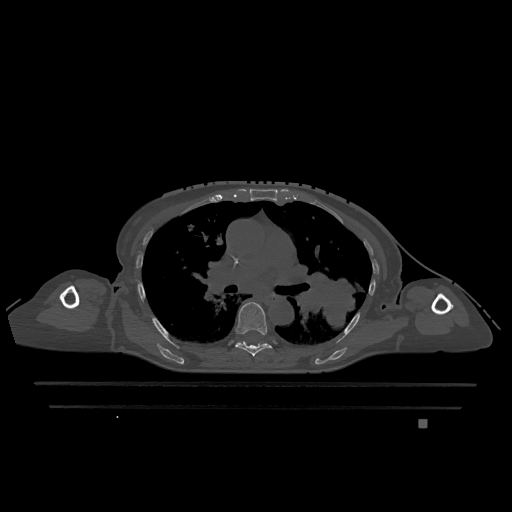
CT including the spine, one axial slice. Slice 784 of 1317 in the series (ordered by position). Bone window (W 1800 / L 400 HU). 512 × 512 image matrix, field of view 500 × 500 mm. Female patient, age 74 years. Case-level facts recorded for this patient, not image findings: primary cancer: lung; vertebrae with lytic lesions (as recorded): T1, T4, T5, T6, L4, L5.
Annotated regions visible in this slice (semi-automatic segmentation, software-assisted and operator-edited):
- T6 vertebra: bounding box (x1, y1, x2, y2) in pixels: (235, 302, 272, 357)